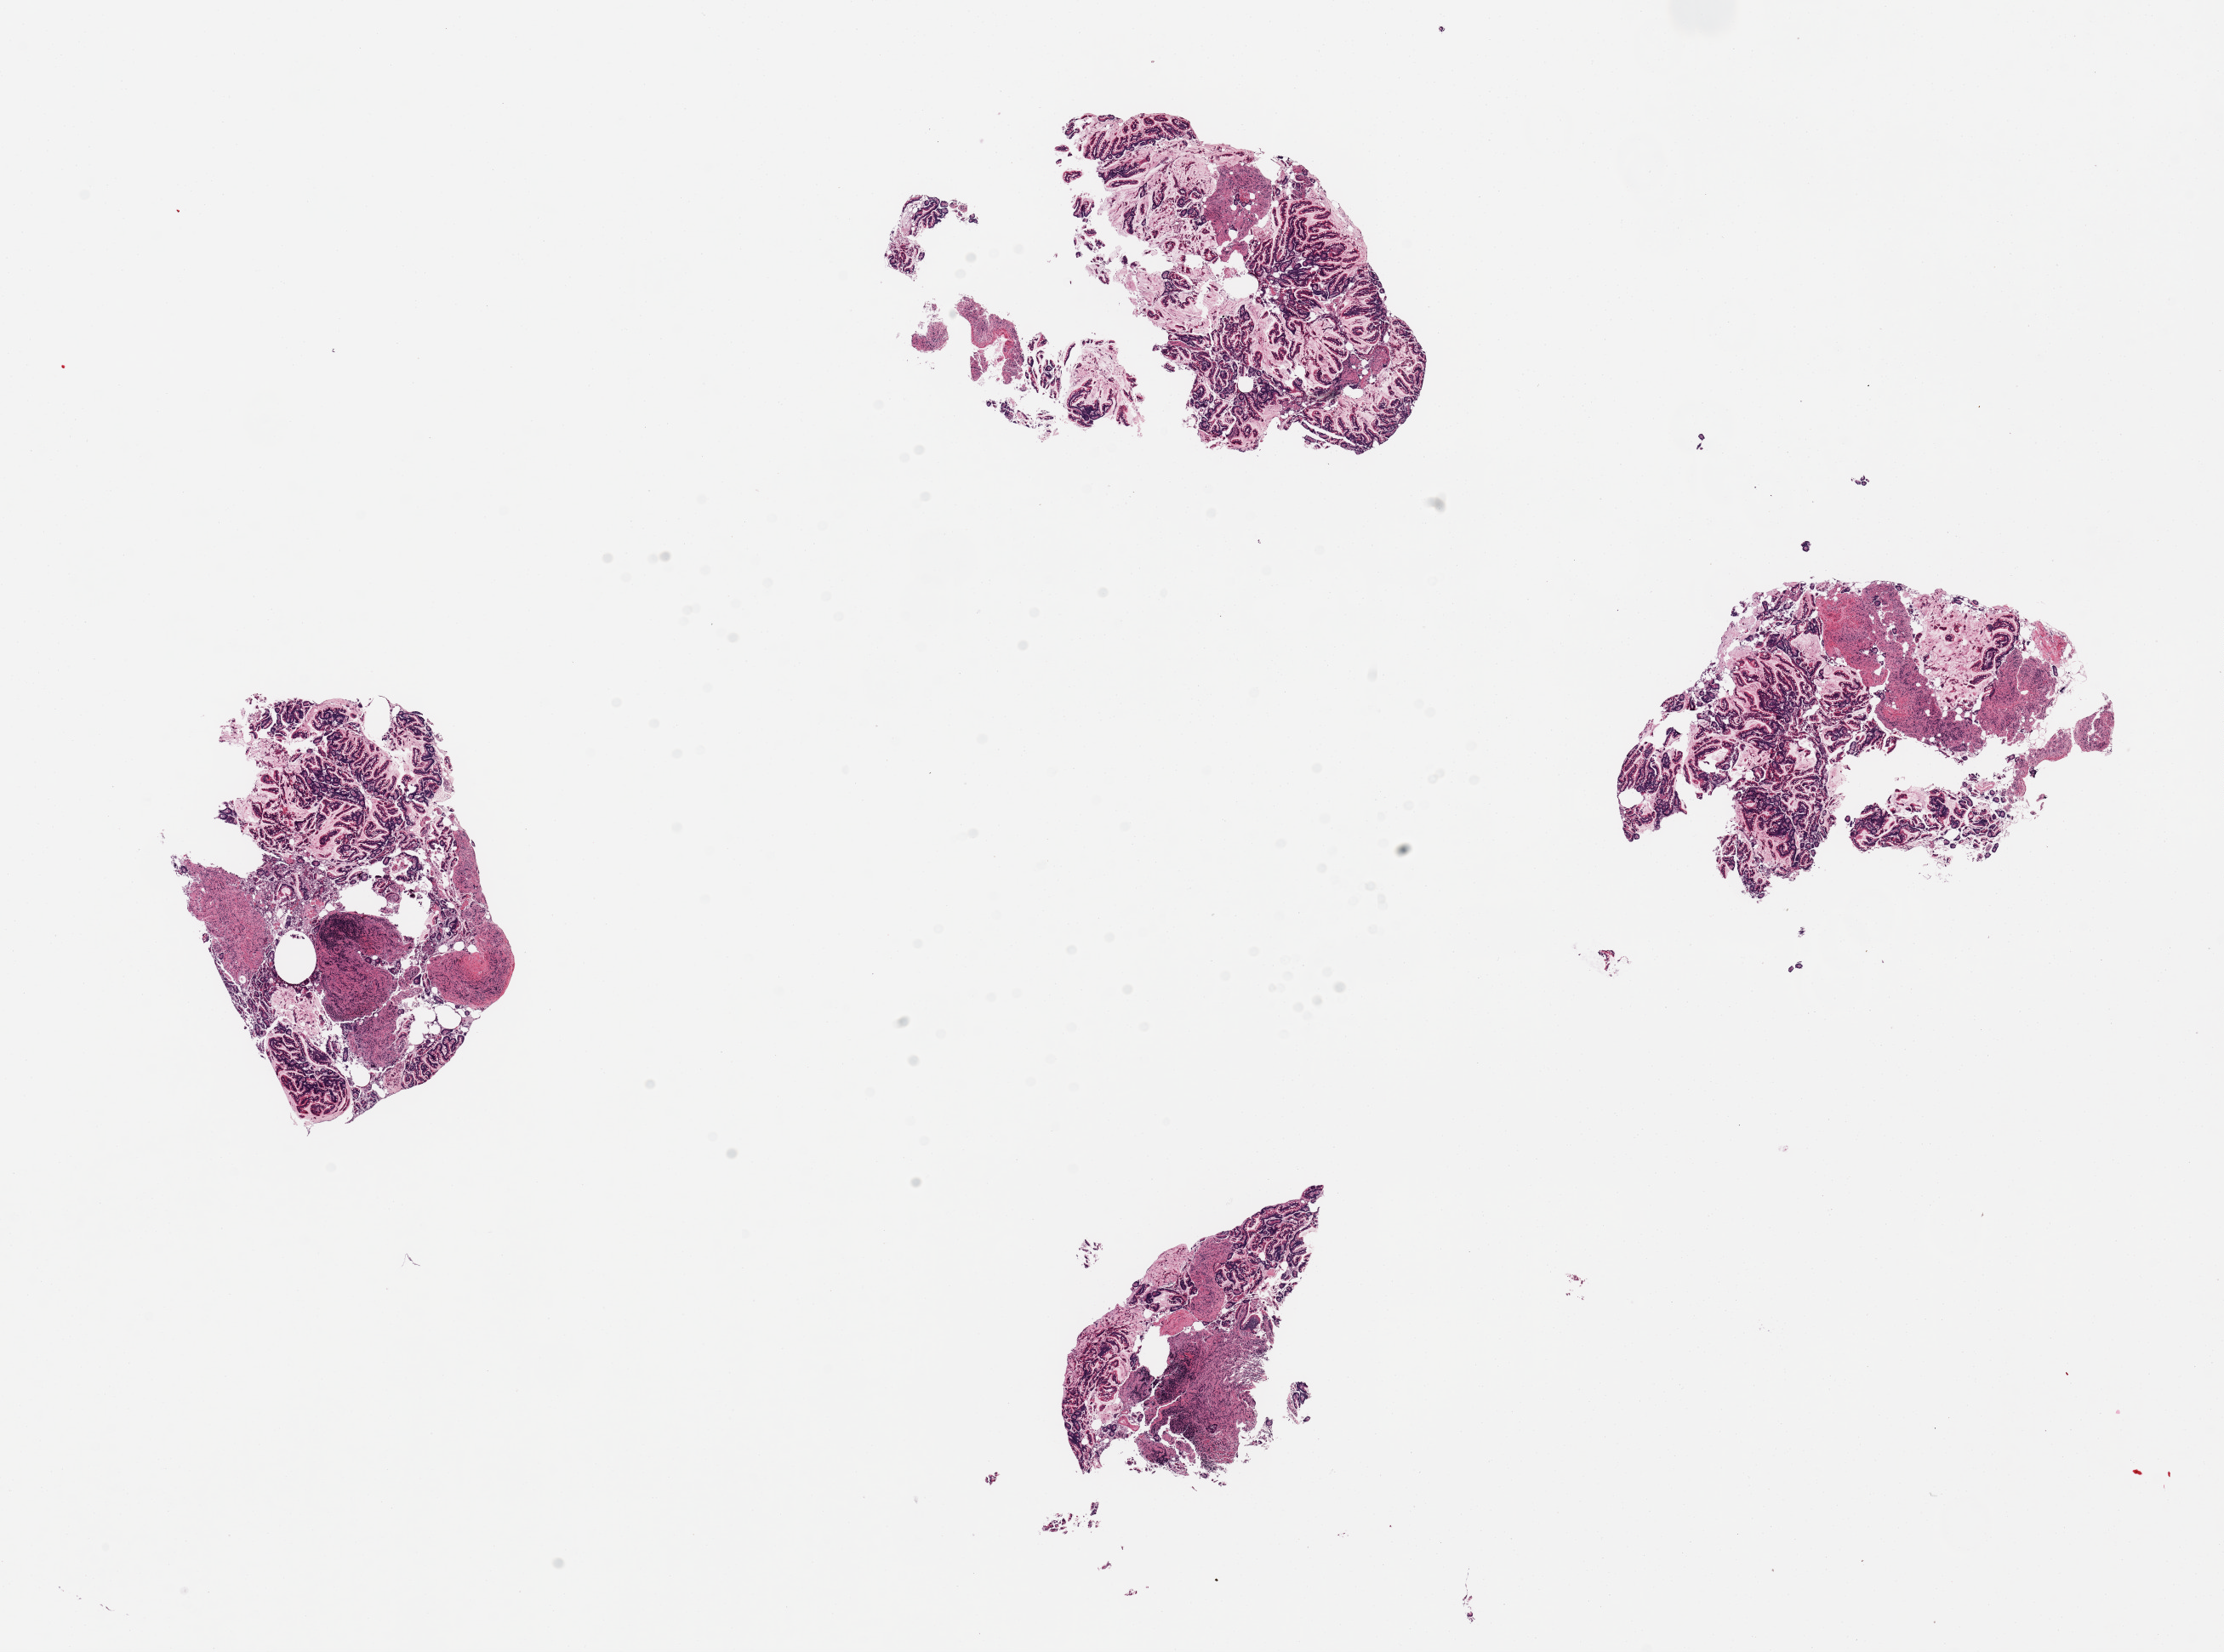
Digitized hematoxylin and eosin (H&E)-stained section, whole scanned area (about 20.7 x 15.4 mm) shown as a low-resolution overview; PAXgene-fixed, paraffin-embedded tissue; target tissue: ileum; donor tissue sample. Female donor.
• review note (as recorded): 4 pieces; minimal lymphoid tissue